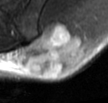
MRI of an extremity soft-tissue mass, one axial slice. Slice 21 of 42 in the series (ordered by position). T2-weighted fat-saturated. MR volume resampled by the dataset authors to the PET/CT grid (not the native acquisition matrix). 3.27 mm slice thickness. 108 × 103 image matrix, field of view 105 × 101 mm. Male patient. From the clinical record (not read from this slice): histological type: leiomyosarcoma; grade: intermediate; site of the primary tumour: left pelvis.
Outlined on this slice (expert contour drawn on MRI and transferred to this co-registered scan by the dataset authors):
- gross tumour volume (mass): box from (x=19, y=21) to (x=86, y=77) px